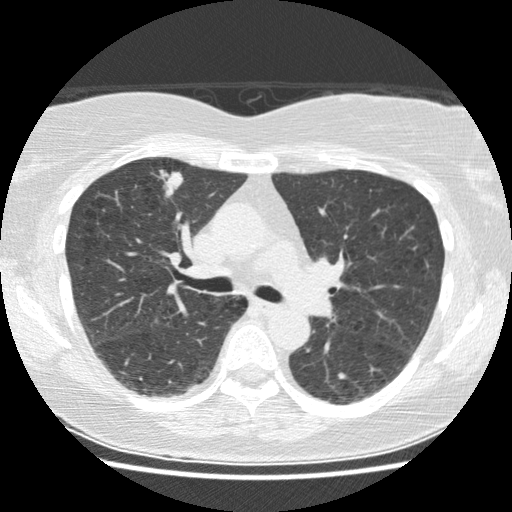
Chest CT (low-dose screening protocol), one axial image, baseline screening round, lung window (W 1500 / L -600 HU), standard (soft-tissue) reconstruction kernel (STANDARD), slice 62 of 155 in the series, 512 × 512 image matrix, field of view 330 × 330 mm. Female participant, aged 63 years at enrolment.
Expert reader's lesion annotation, bounding box <146,155,190,210> (left, top, right, bottom; pixels). The exam's reader record, not a measurement of the box and not confirmed to be the same lesion: non-calcified nodule or mass ≥4 mm, right upper lobe, 18 × 14 mm, spiculated (stellate) margins, soft tissue attenuation. Participant outcome: lung cancer diagnosed 87 days after this screen — papillary adenocarcinoma, NOS, right upper lobe, well differentiated (G1), stage IA (AJCC 6th edition), 19 mm at pathology.